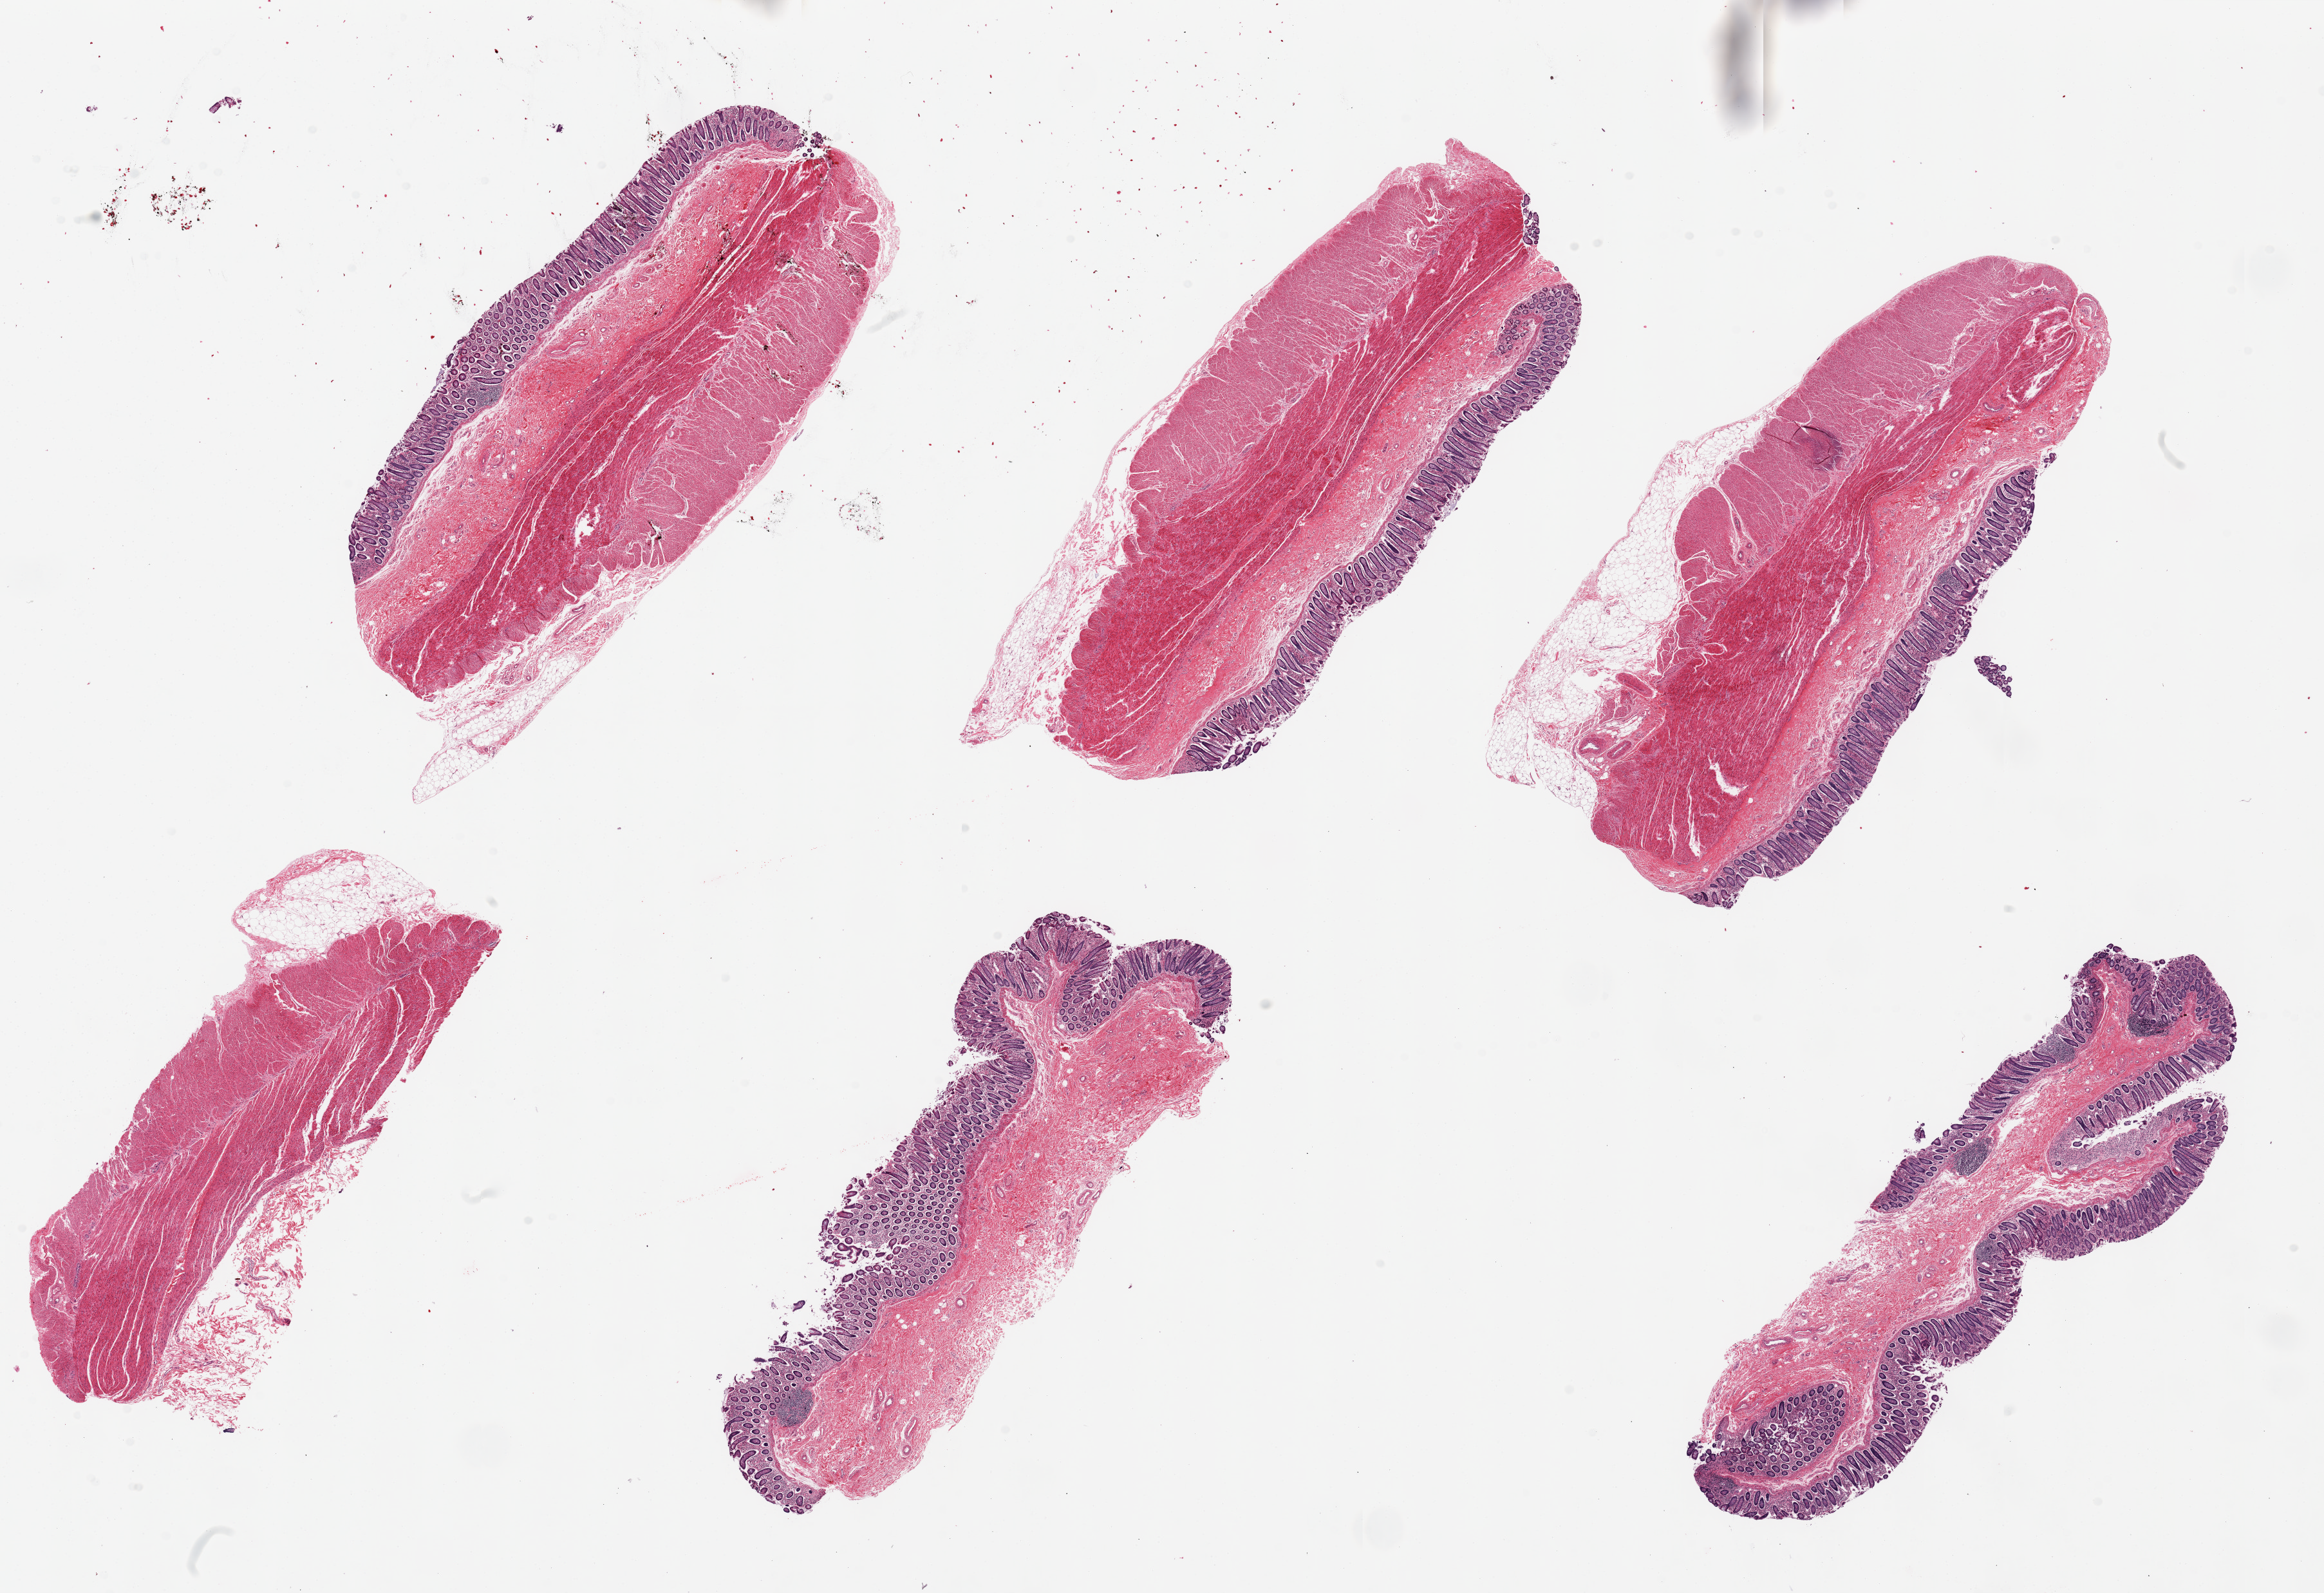
Whole-slide image, hematoxylin and eosin (H&E) stain, low-resolution overview of the scanned area, about 28.5 x 19.6 mm, PAXgene-fixed paraffin-embedded (PFPE) section, sampled site (target tissue): transverse colon, tissue donor sample. Donor sex: male.
Review note (as recorded): 6 pieces ~7x4mm, mucosa moderately autoyzed, 10-20% of thickness.